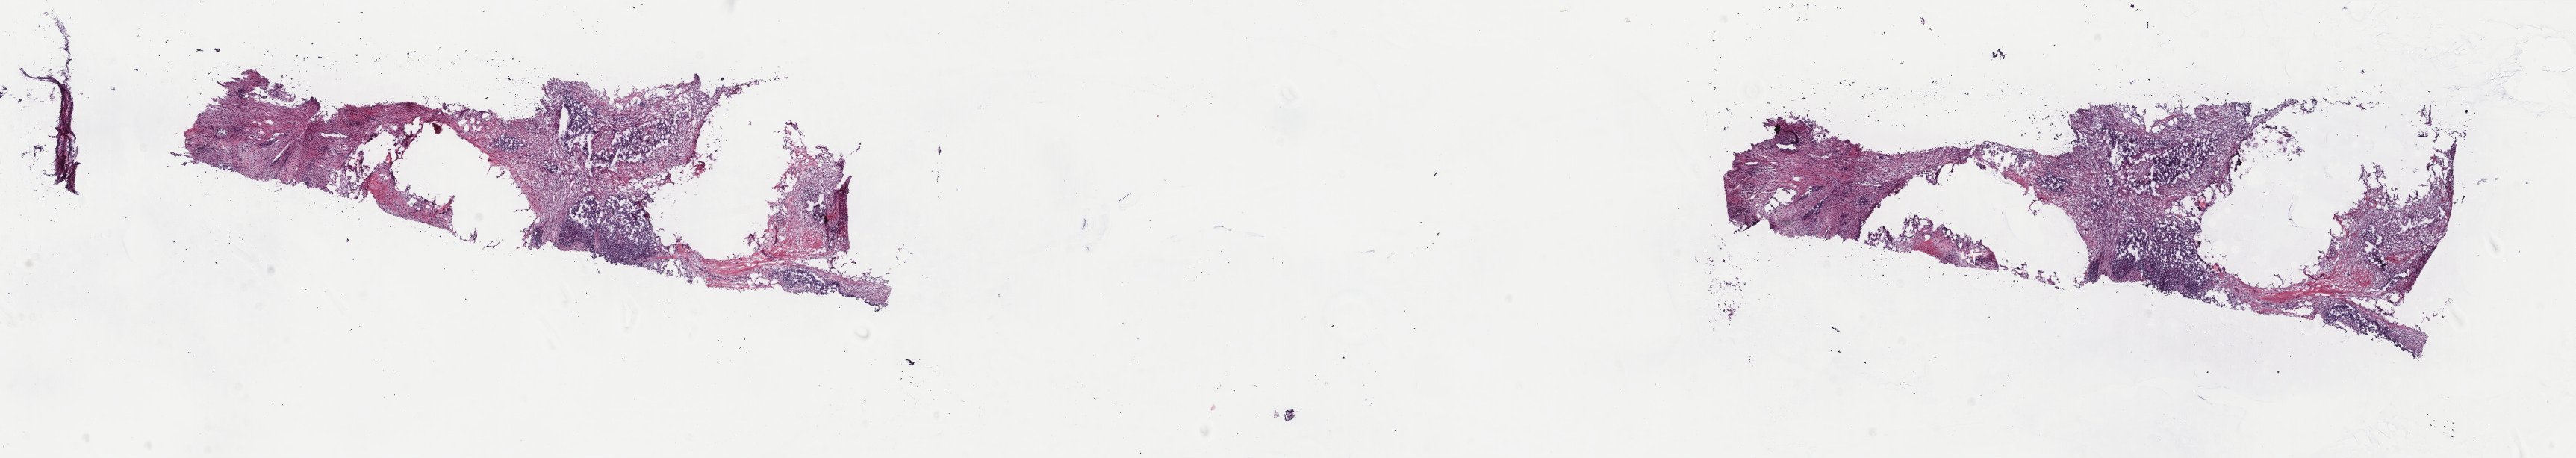
H&E-stained whole-slide image, whole scanned area (about 27.4 x 4.9 mm) shown as a low-resolution overview; frozen section from the top of the tissue portion; primary tumour sample from the uterus. Female patient; age at initial diagnosis 80 years. Composition of this section per pathologist review: tumour cells 100%, tumour nuclei 80%, normal cells 0%, stromal cells 0%, necrosis 0%. Inflammatory infiltration, as recorded: lymphocyte infiltration 2%, monocyte infiltration 0%, neutrophil infiltration 0%.
- pathologic diagnosis: Carcinosarcoma, NOS (fundus uteri)
- FIGO stage: IVB